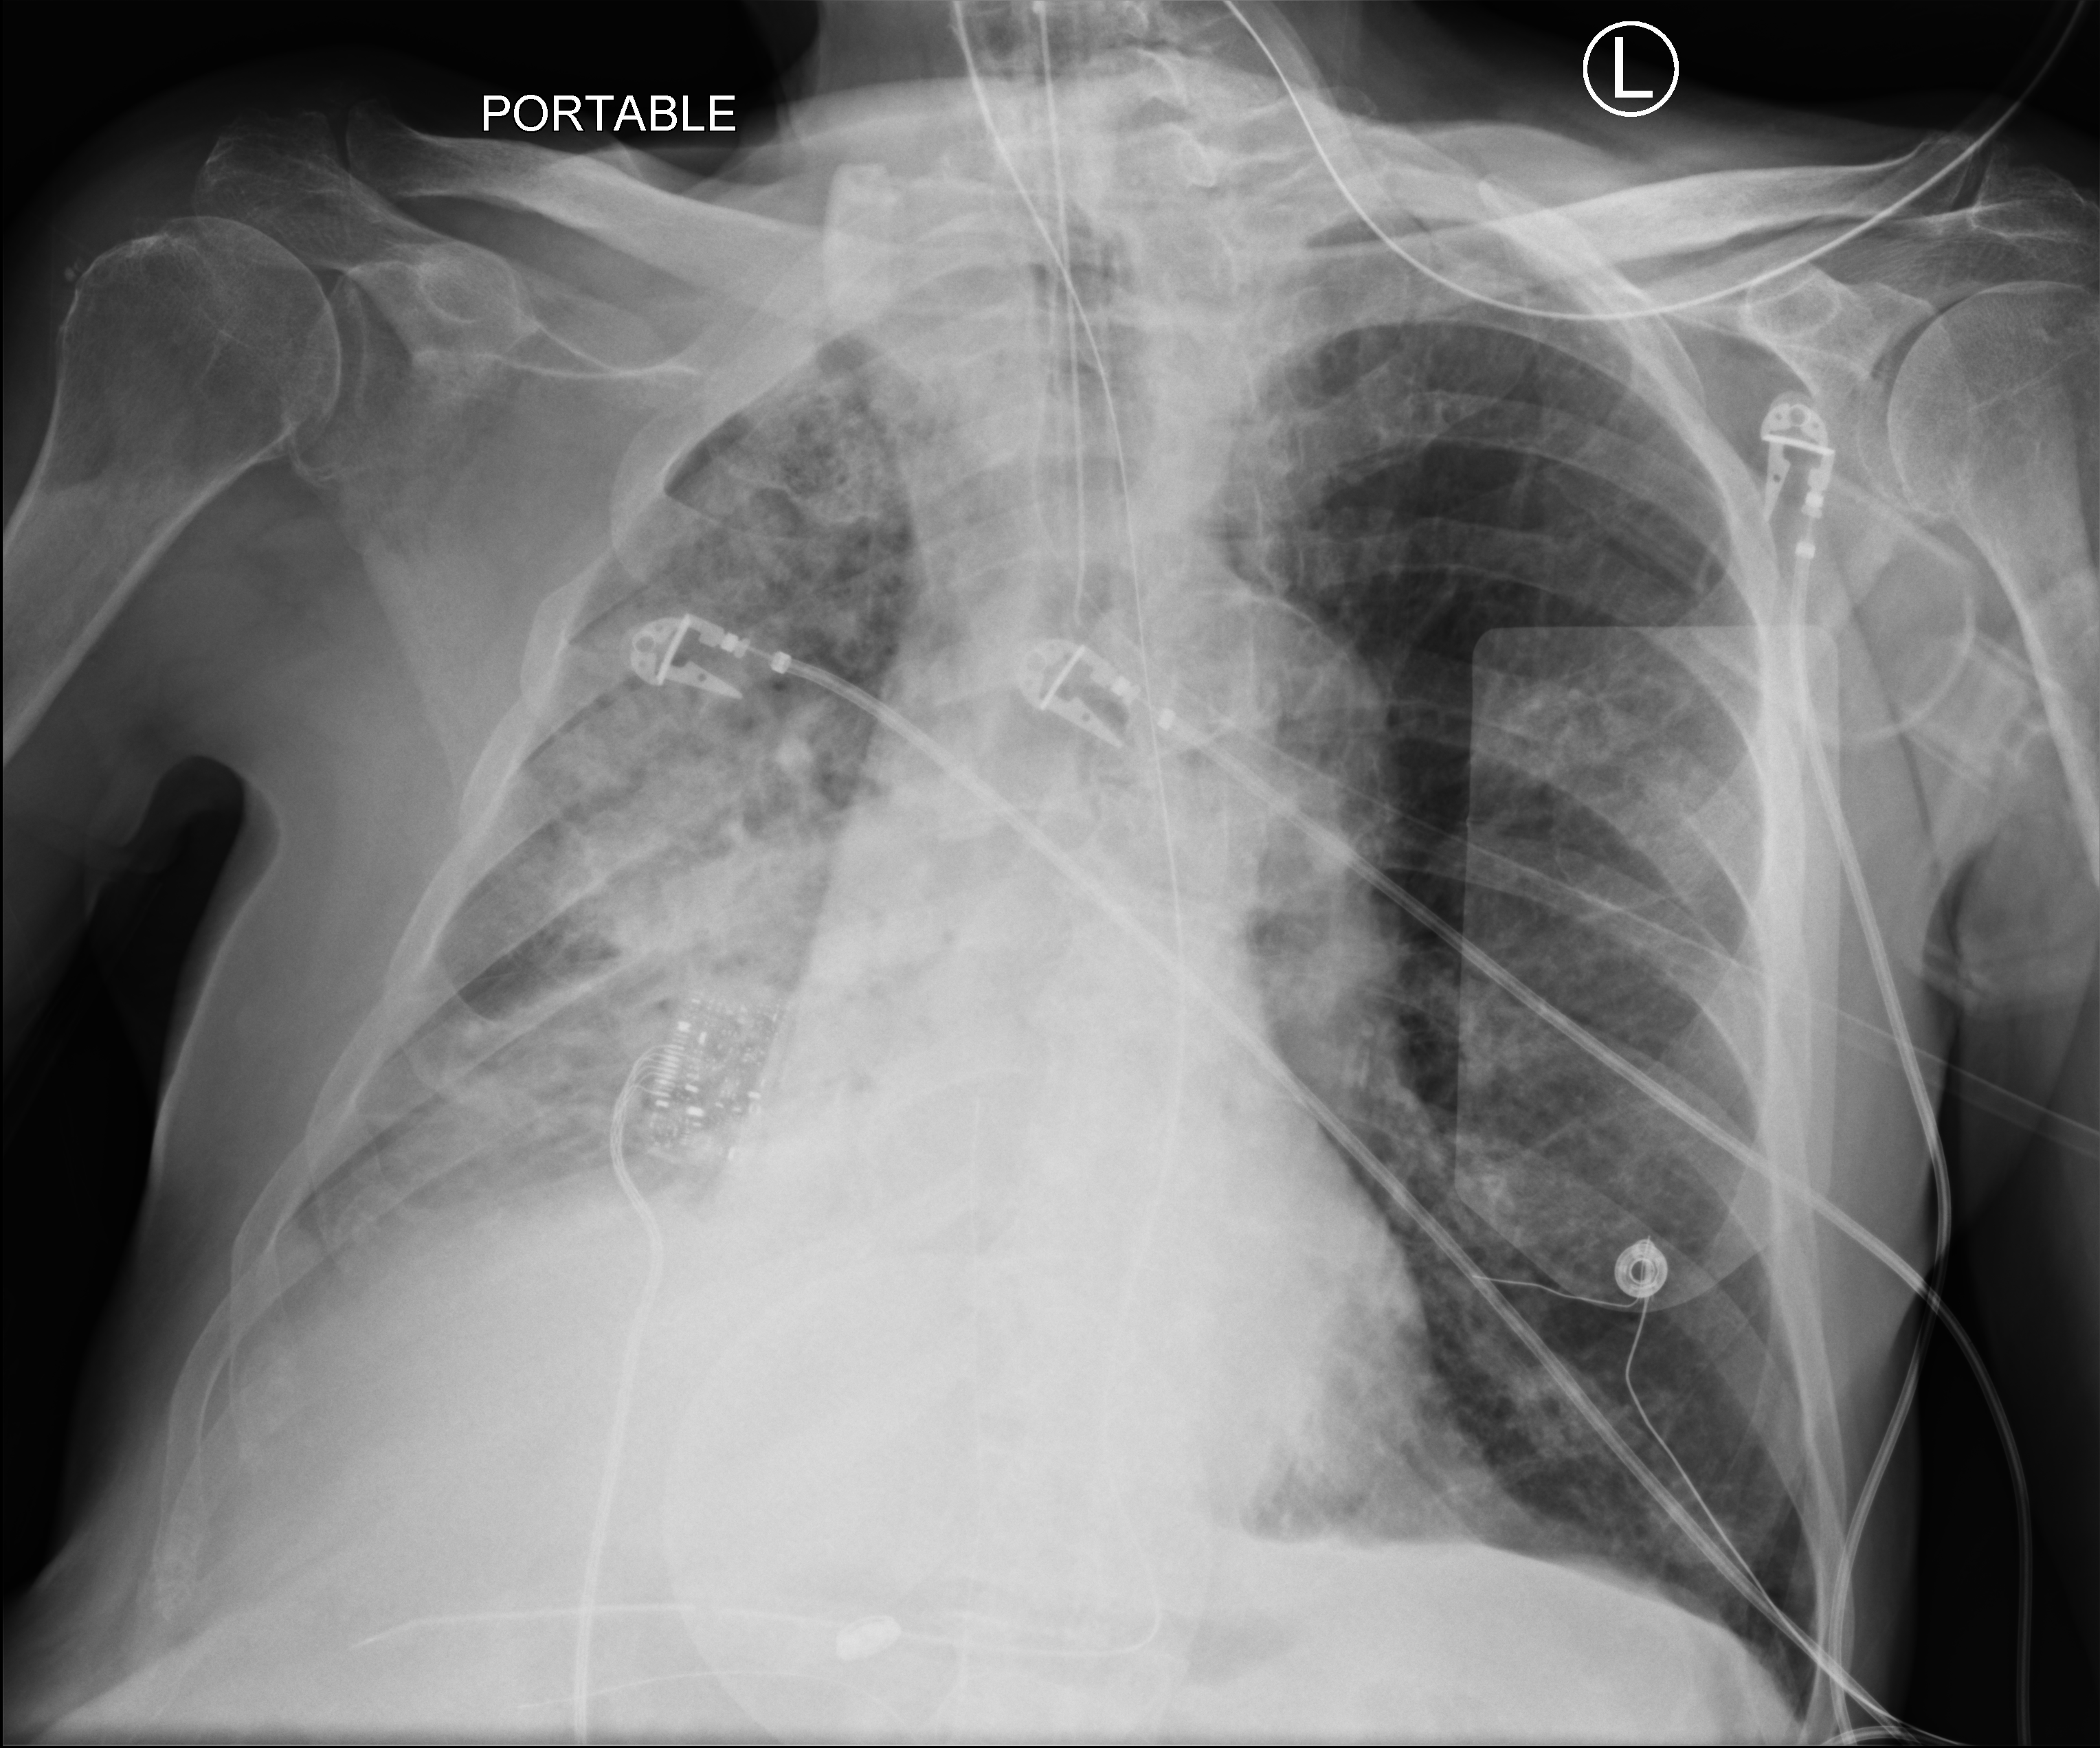
Bedside chest radiograph (computed radiography); anteroposterior (AP) projection. Male patient hospitalised with COVID-19, age 75–90 years.
Hospital-stay facts (about this admission, not read from this image; timing relative to this image not recorded): admitted to intensive care during this hospital stay: yes; mechanically ventilated during this hospital stay: yes; length of hospital stay: 28 days.